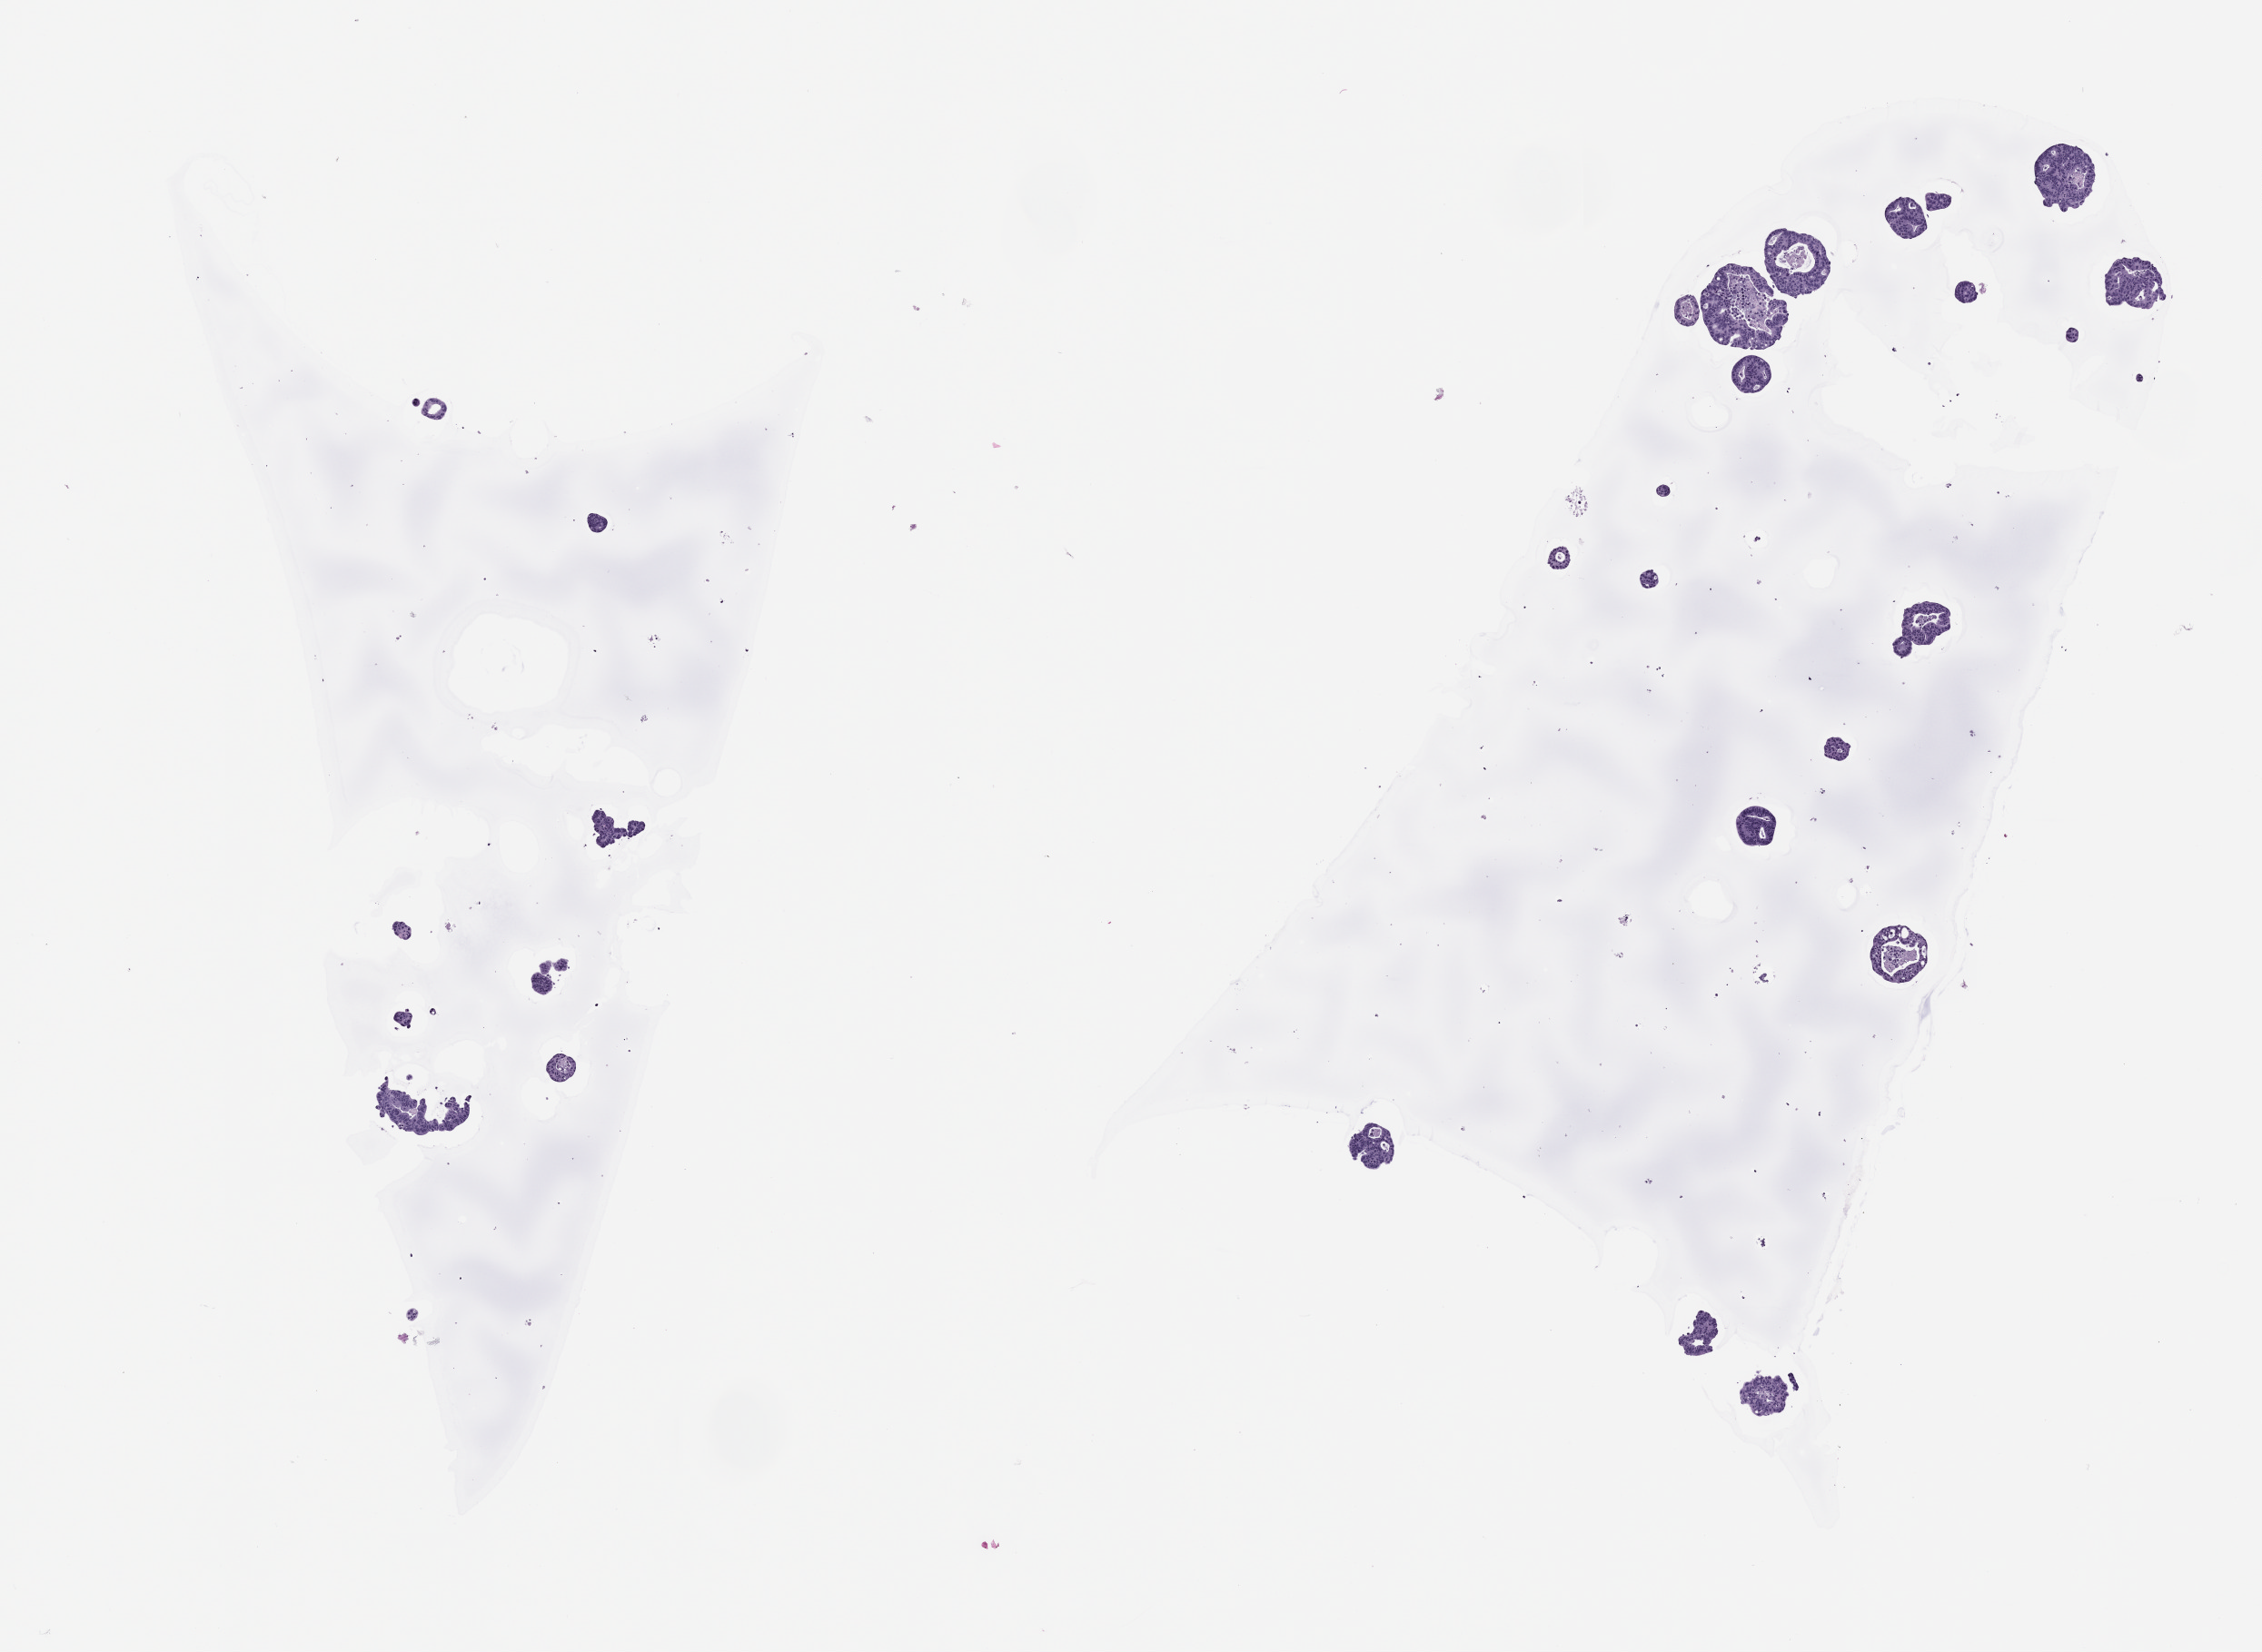
Whole-slide image, haematoxylin and eosin: patient-derived xenograft (human tumor grown in a mouse), passage 0, whole scanned area (about 10.0 x 7.3 mm) shown as a low-resolution overview. Formalin-fixed paraffin-embedded section. Originating tumor site category: rectum.
- originating patient diagnosis: Rectal Adenocarcinoma